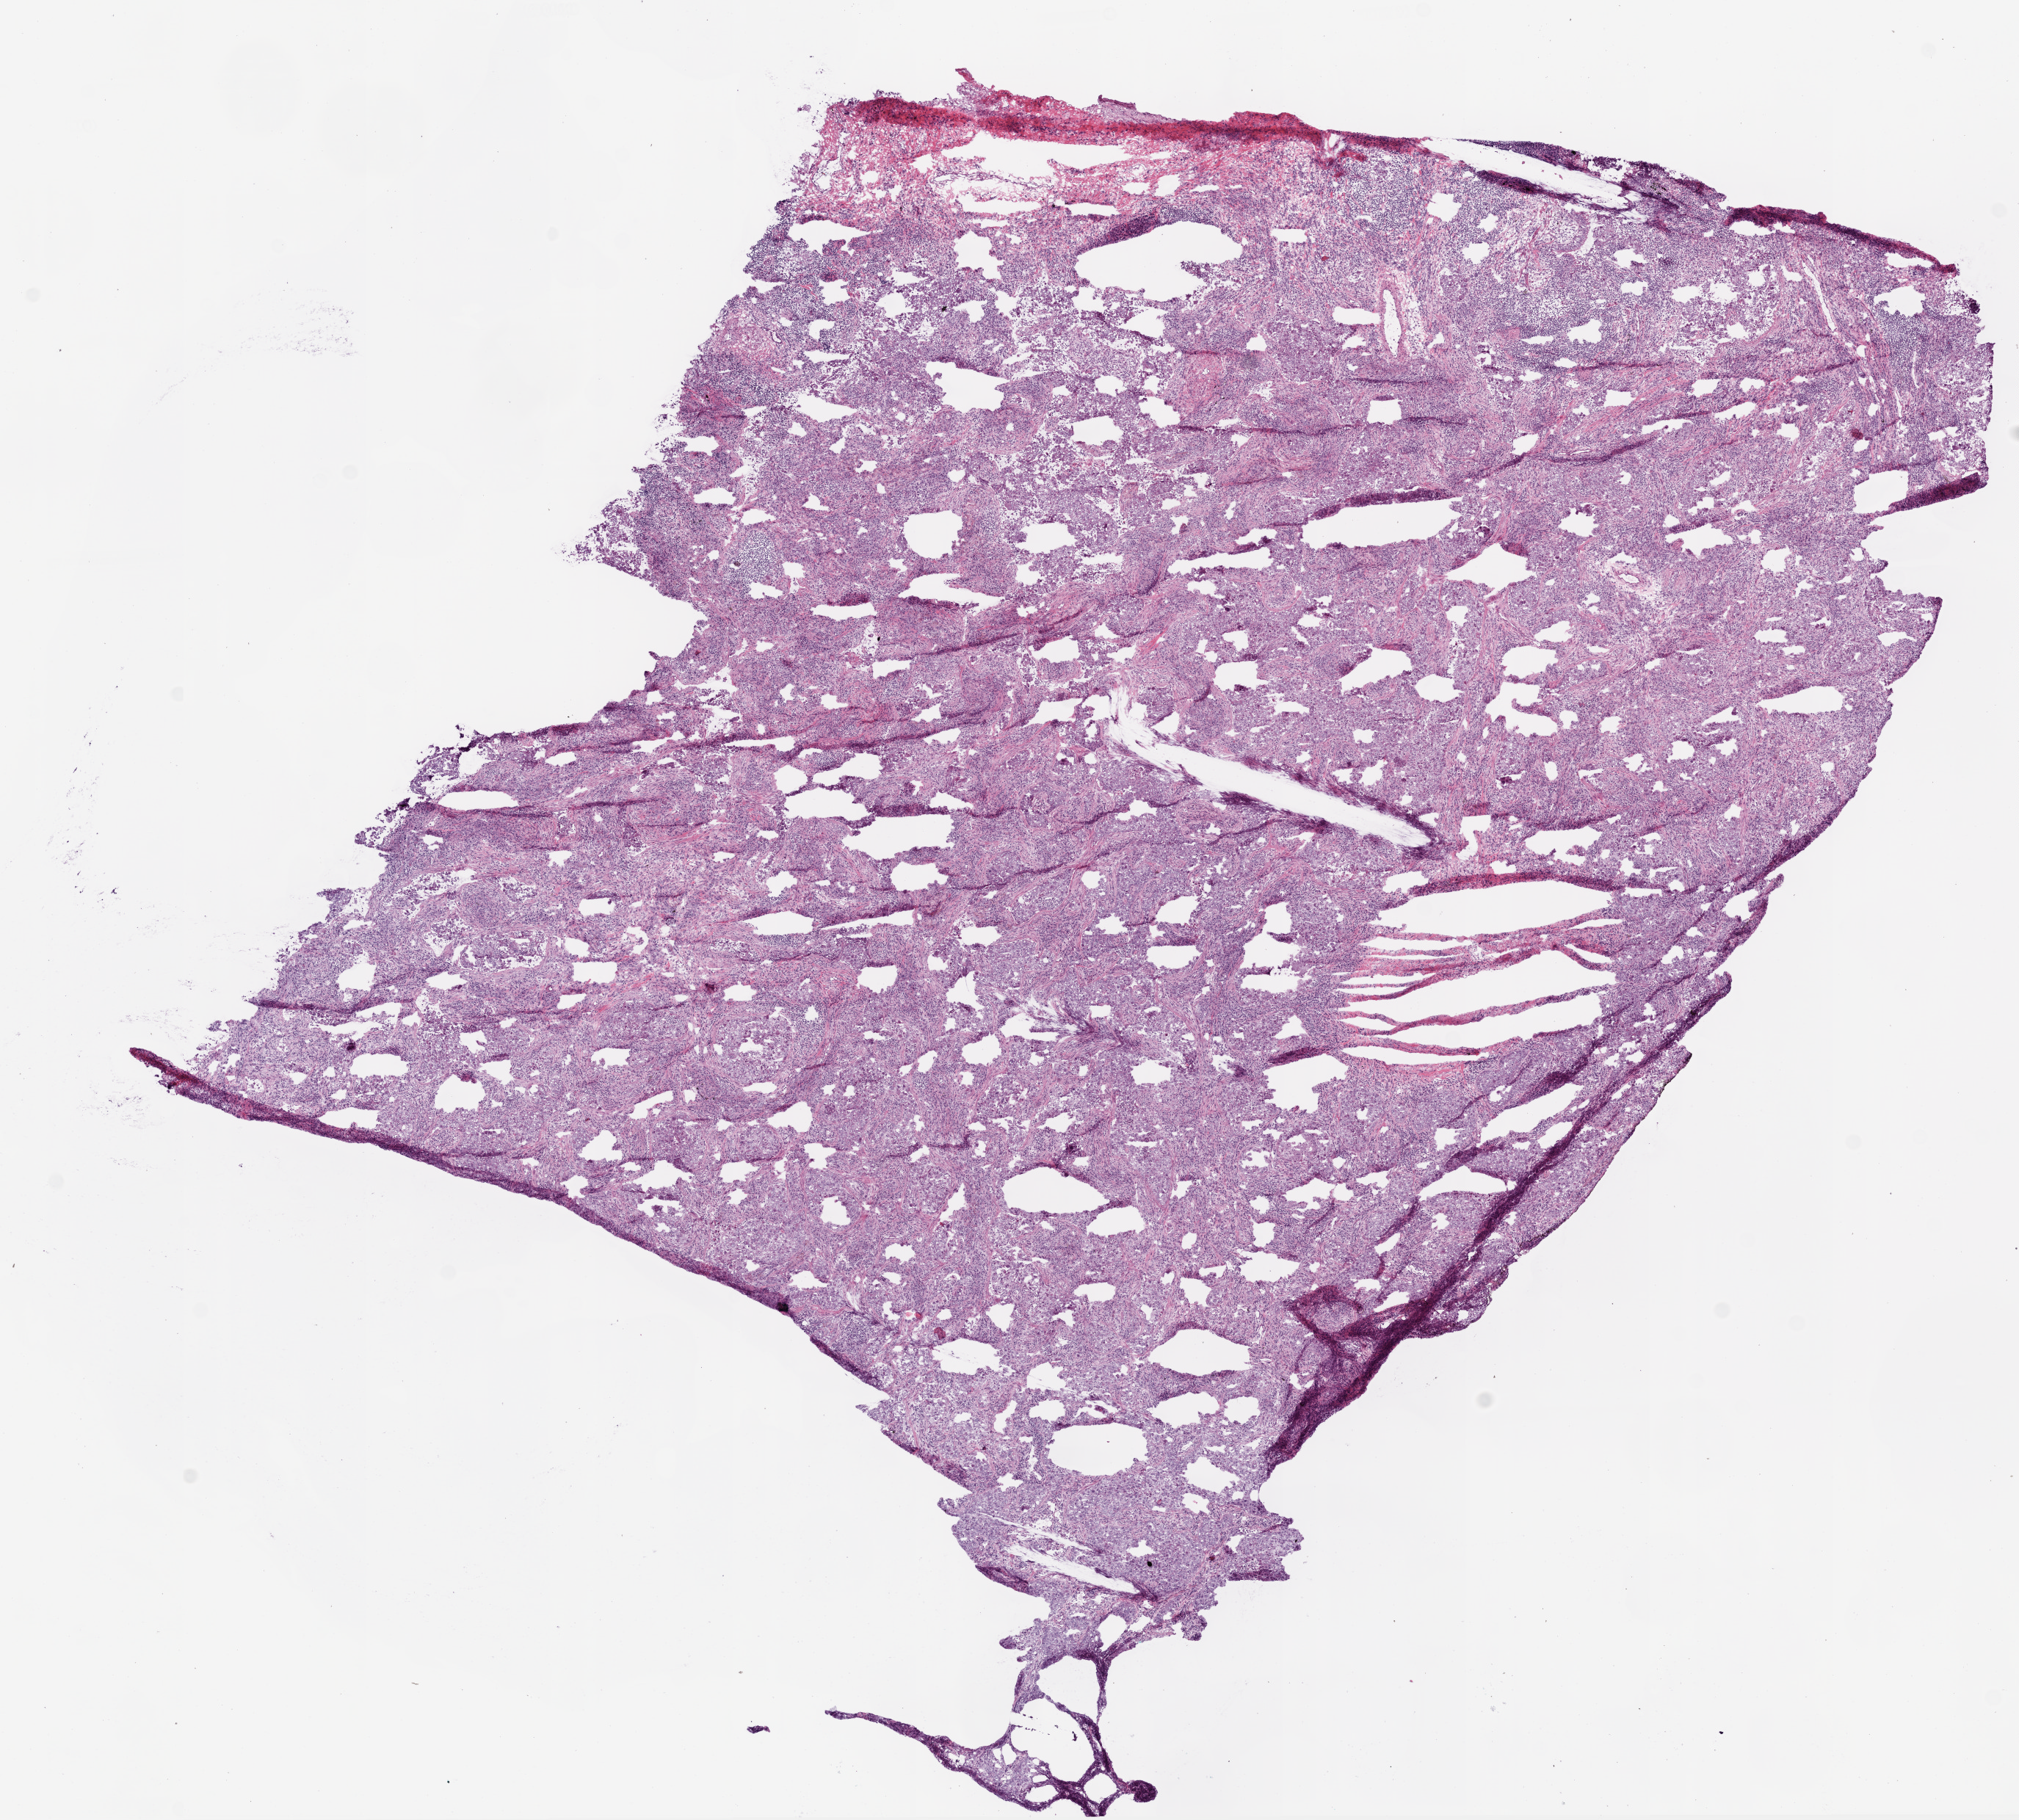
Digitized H&E-stained tissue section (whole slide), whole scanned area (about 11.0 x 9.9 mm, acquisition: 20x scan) shown as a low-resolution overview. Frozen section from the bottom of the tissue portion. Lung, primary tumour sample. Female patient; age at initial diagnosis 74 years. Composition of this section per pathologist review: tumour cells 80%, tumour nuclei 75%, stromal cells 15%, necrosis 5%. Infiltration values recorded for this section: lymphocyte infiltration 15%.
Histologic diagnosis: Adenocarcinoma, NOS (upper lobe, lung). AJCC pathologic stage: IIIA (7th edition).